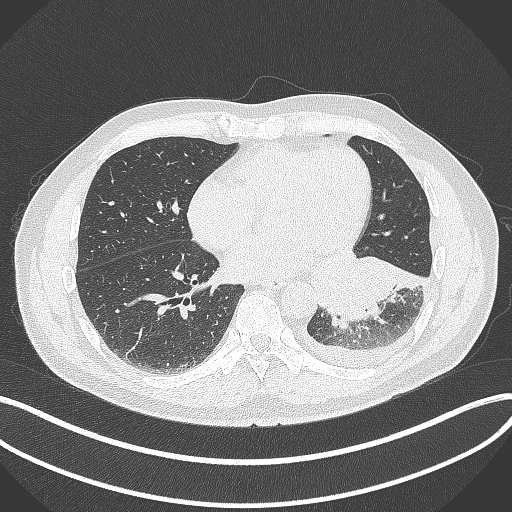
Chest CT, one axial slice. Position 140 of 342 along the scan axis. Reconstruction kernel B70f. 120 kVp. Lung window (W 1500 / L -600 HU). 1 mm slice thickness. 512 × 512 image matrix, field of view 400 × 400 mm. Male patient, age 58 years. From the clinical record (not read from this slice): clinical TNM (as recorded): T3 N1 M1b; histopathological grade: G3.
Structures marked on this image (bounding box drawn by a radiologist):
- lung tumour (recorded histology: small cell carcinoma): bounding box [x1, y1, x2, y2] px = [301, 244, 426, 328]